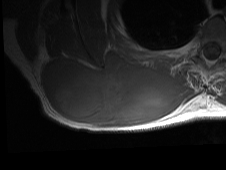
MRI of an extremity soft-tissue mass, one axial slice. MR volume resampled by the dataset authors to the PET/CT grid (not the native acquisition matrix). 3.27 mm slice thickness. 226 × 170 image matrix, field of view 221 × 166 mm. Male patient. Case-level facts recorded for this patient, not image findings: histological type: pleiomorphic spindle cell undifferentiated; grade: high; site of the primary tumour: right parascapusular.
Structures marked on this image (expert contour drawn on MRI and transferred to this co-registered scan by the dataset authors):
- gross tumour volume including surrounding oedema: bounding box <42,49,193,128> (left, top, right, bottom; pixels)
- gross tumour volume (mass): <42,49,175,125>